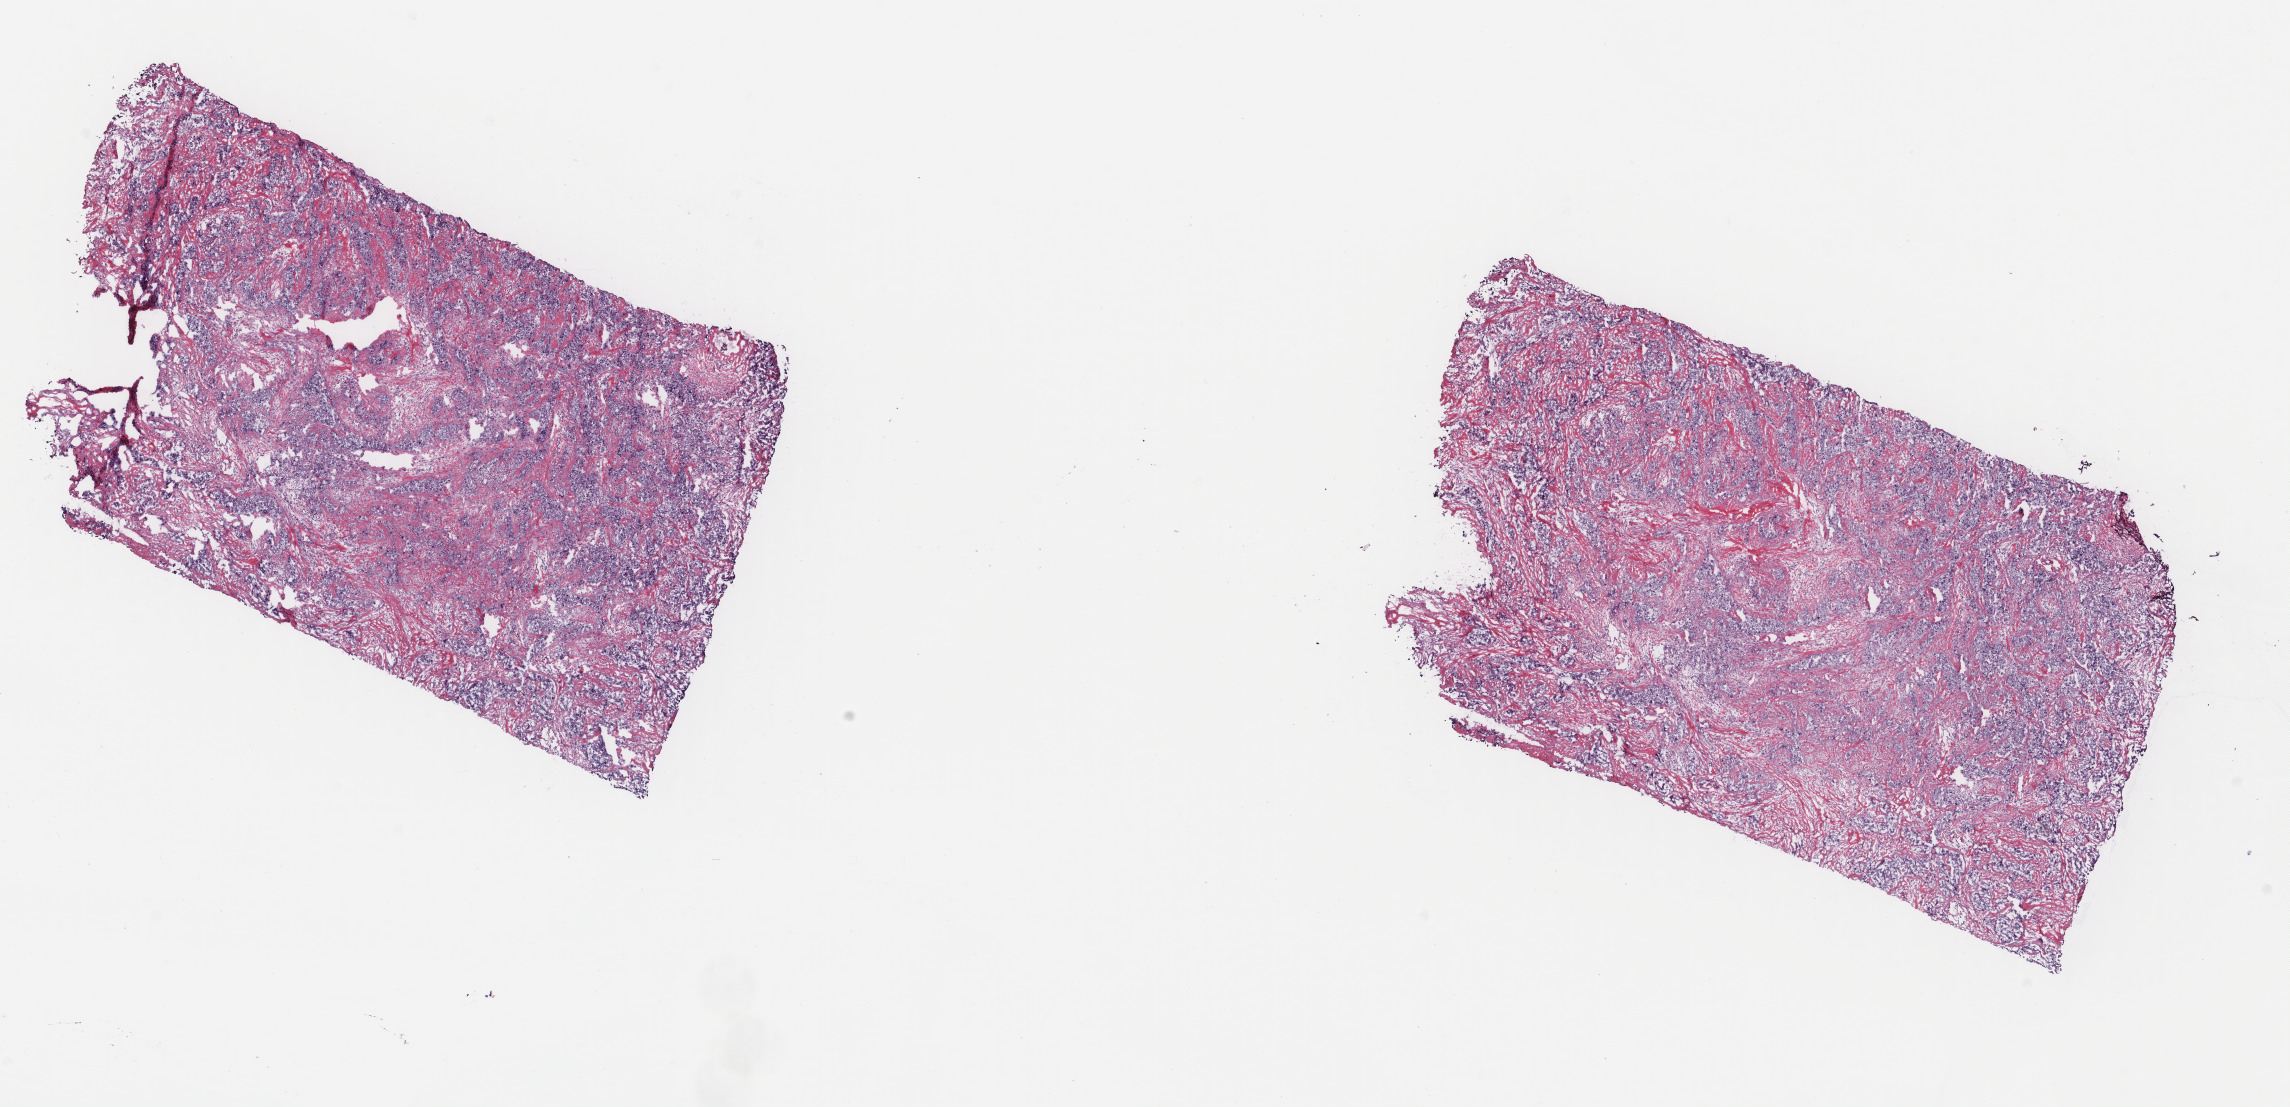
Whole-slide histology image, H&E, shown as a low-resolution overview of the whole scanned area (about 18.2 x 8.8 mm). Frozen section. Sample: primary tumour, breast. Female, age 65 years at initial diagnosis. Slide review estimates, as recorded: tumour cells 70%, tumour nuclei 80%, normal cells 0%, stromal cells 30%, necrosis 0%. Inflammatory infiltration, as recorded: lymphocyte infiltration 0%, monocyte infiltration 0%, neutrophil infiltration 0%.
AJCC pathologic stage: IIA. Pathologic diagnosis: Infiltrating duct carcinoma, NOS. Laterality: left.